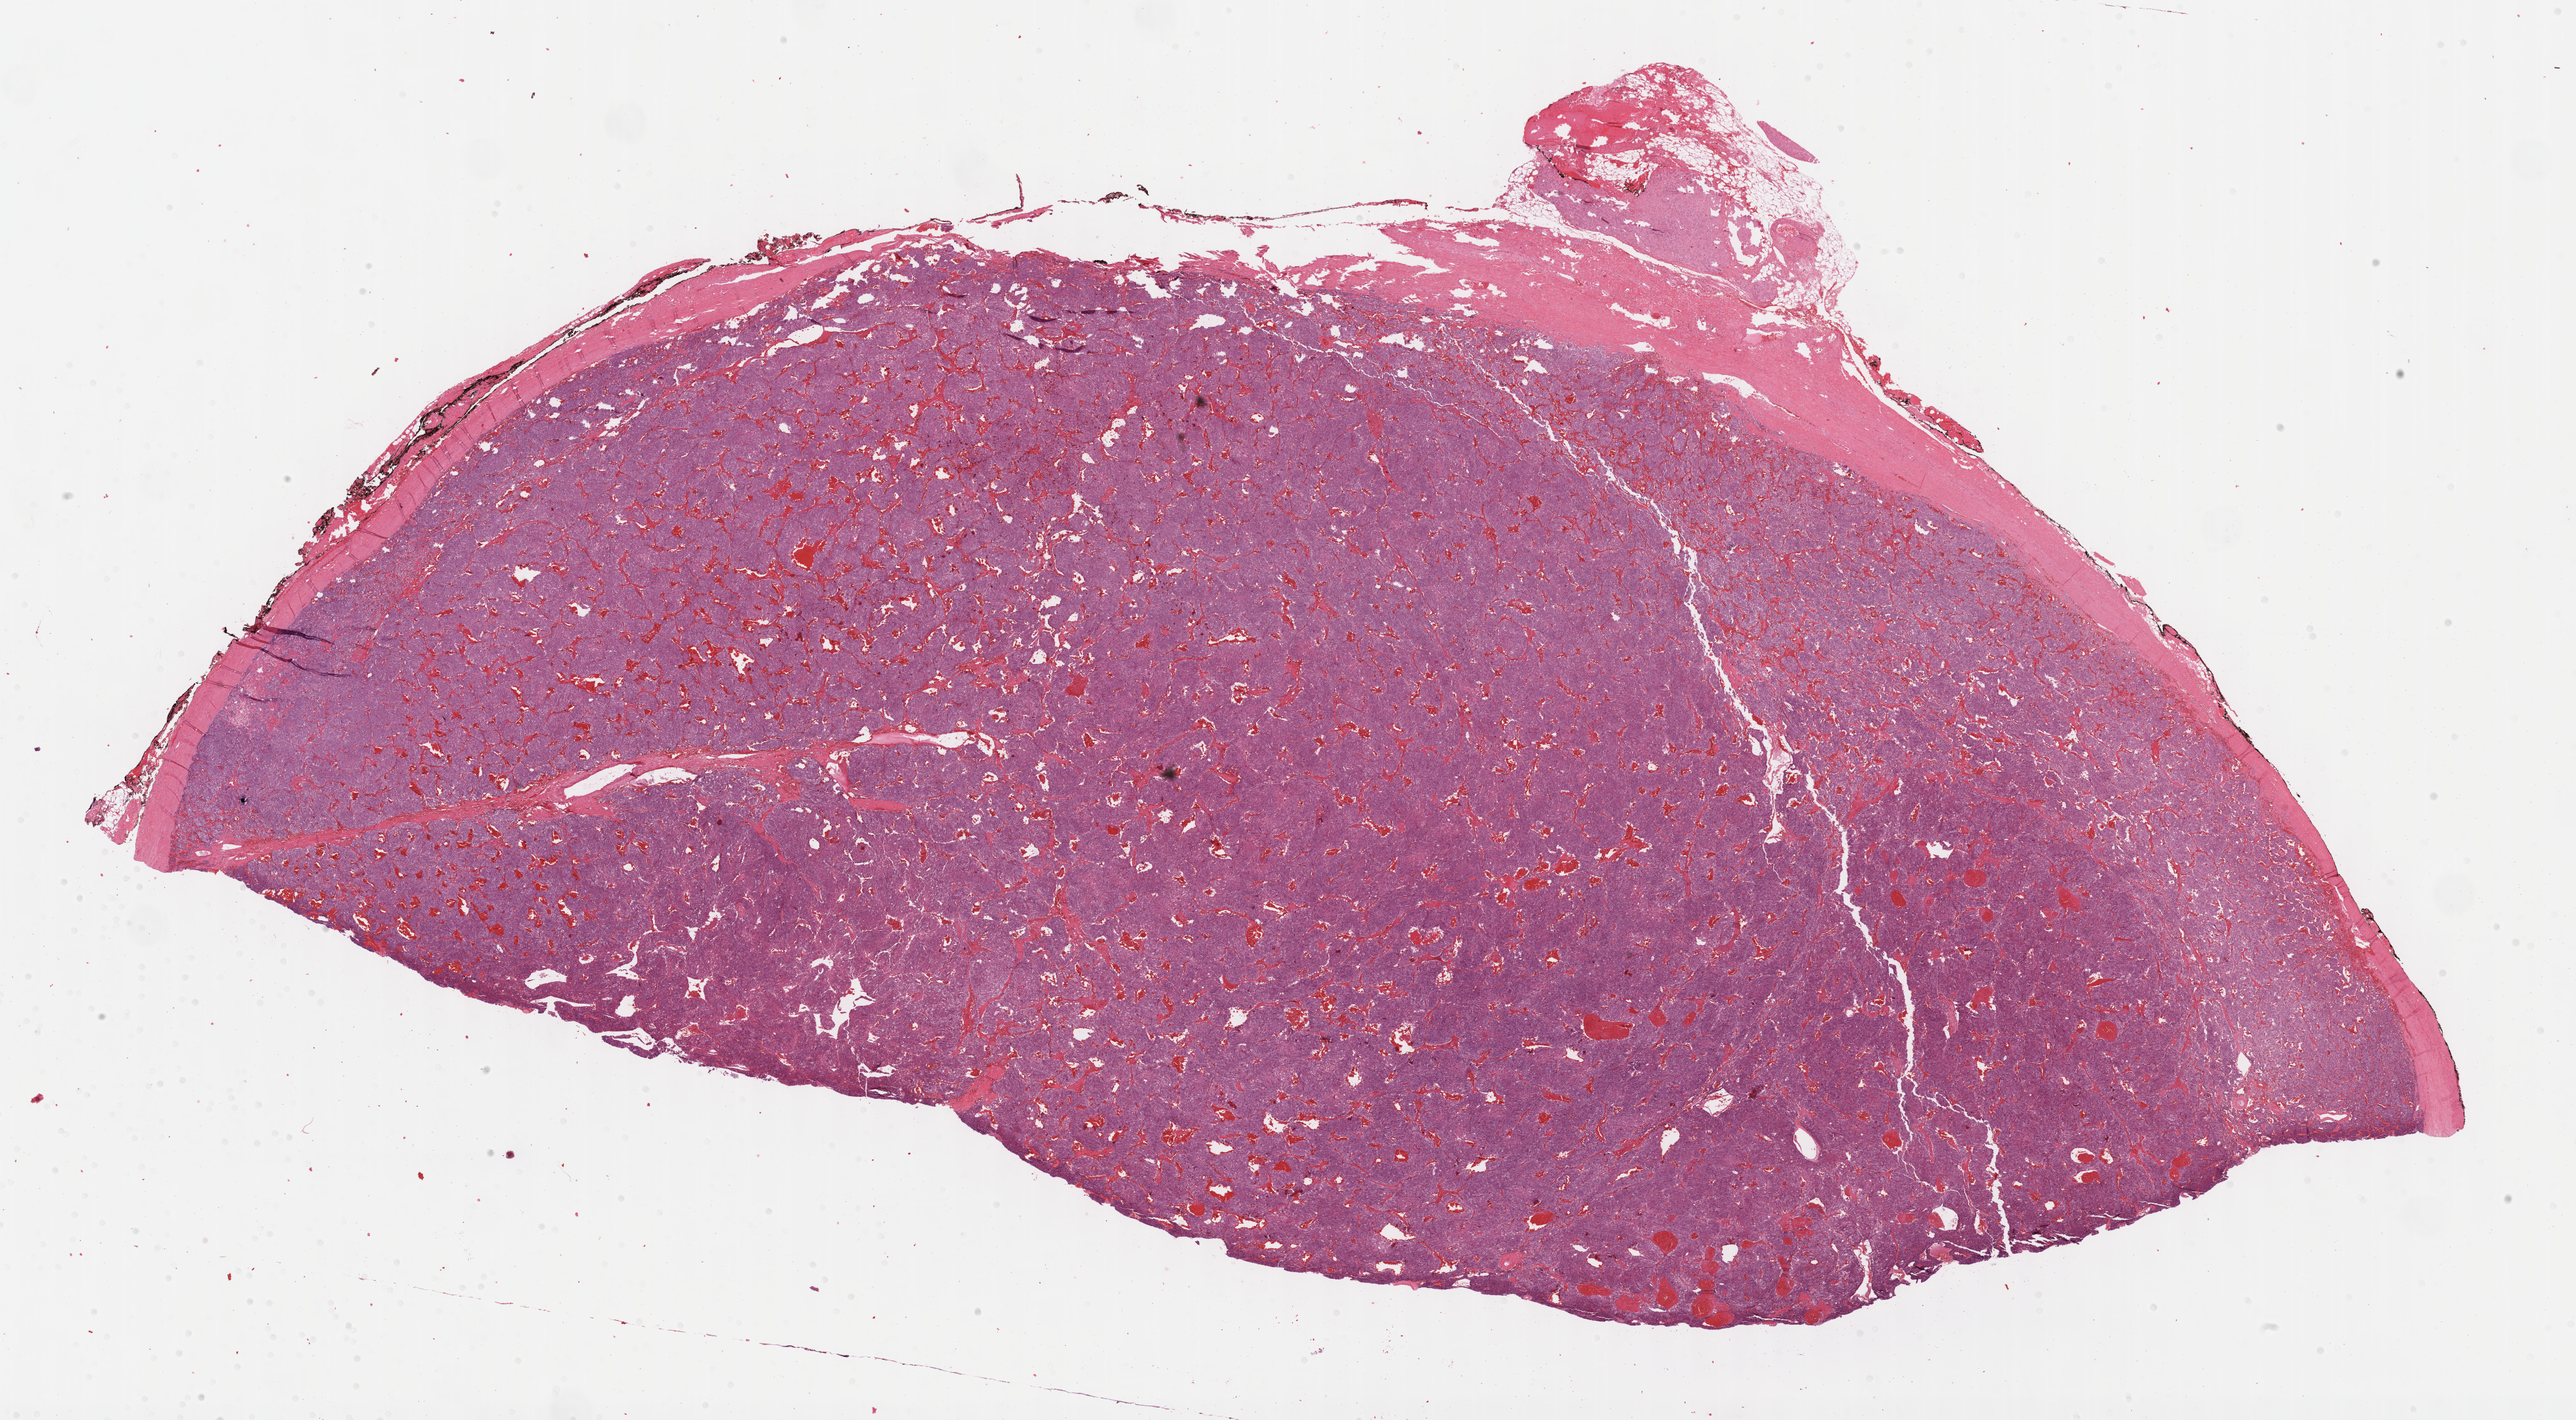
H&E-stained whole-slide image — low-resolution overview of the scanned area, about 31.7 x 17.5 mm (from a 40x scan); formalin-fixed paraffin-embedded (FFPE) diagnostic section; primary tumour sample from the adrenal gland. Female patient; age at initial diagnosis 63 years.
• laterality: right
• histologic diagnosis: Pheochromocytoma, NOS